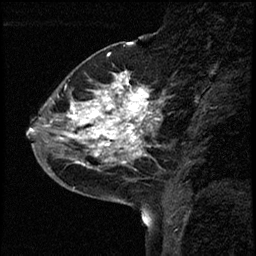
Breast MRI (dynamic contrast-enhanced), one sagittal slice. Slice 20 of 68 in the series (ordered by position). Dynamic contrast-enhanced study with each time point stored as its own series, time point 2 of 3 at this slice position (early post-contrast, ordered by acquisition time). 1.5 T. TE 4.2 ms, TR 17.6 ms. 2 mm slice thickness. 256 × 256 image matrix, field of view 200 × 200 mm. Patient: female, 52 years. Case-level facts recorded for this patient, not image findings: setting: breast cancer imaged before/during neoadjuvant chemotherapy; receptor status: HER2-positive.
Annotated regions visible in this slice (semi-automatic segmentation, software-assisted and operator-edited):
- analysis volume of interest (the breast-tissue region the enhancement analysis was run in; not a lesion): bounding box (x1, y1, x2, y2) in pixels: (50, 61, 165, 184)
- tumour enhancement mask (voxels above the 100 % enhancement threshold inside the analysis volume of interest): (50, 74, 158, 166)